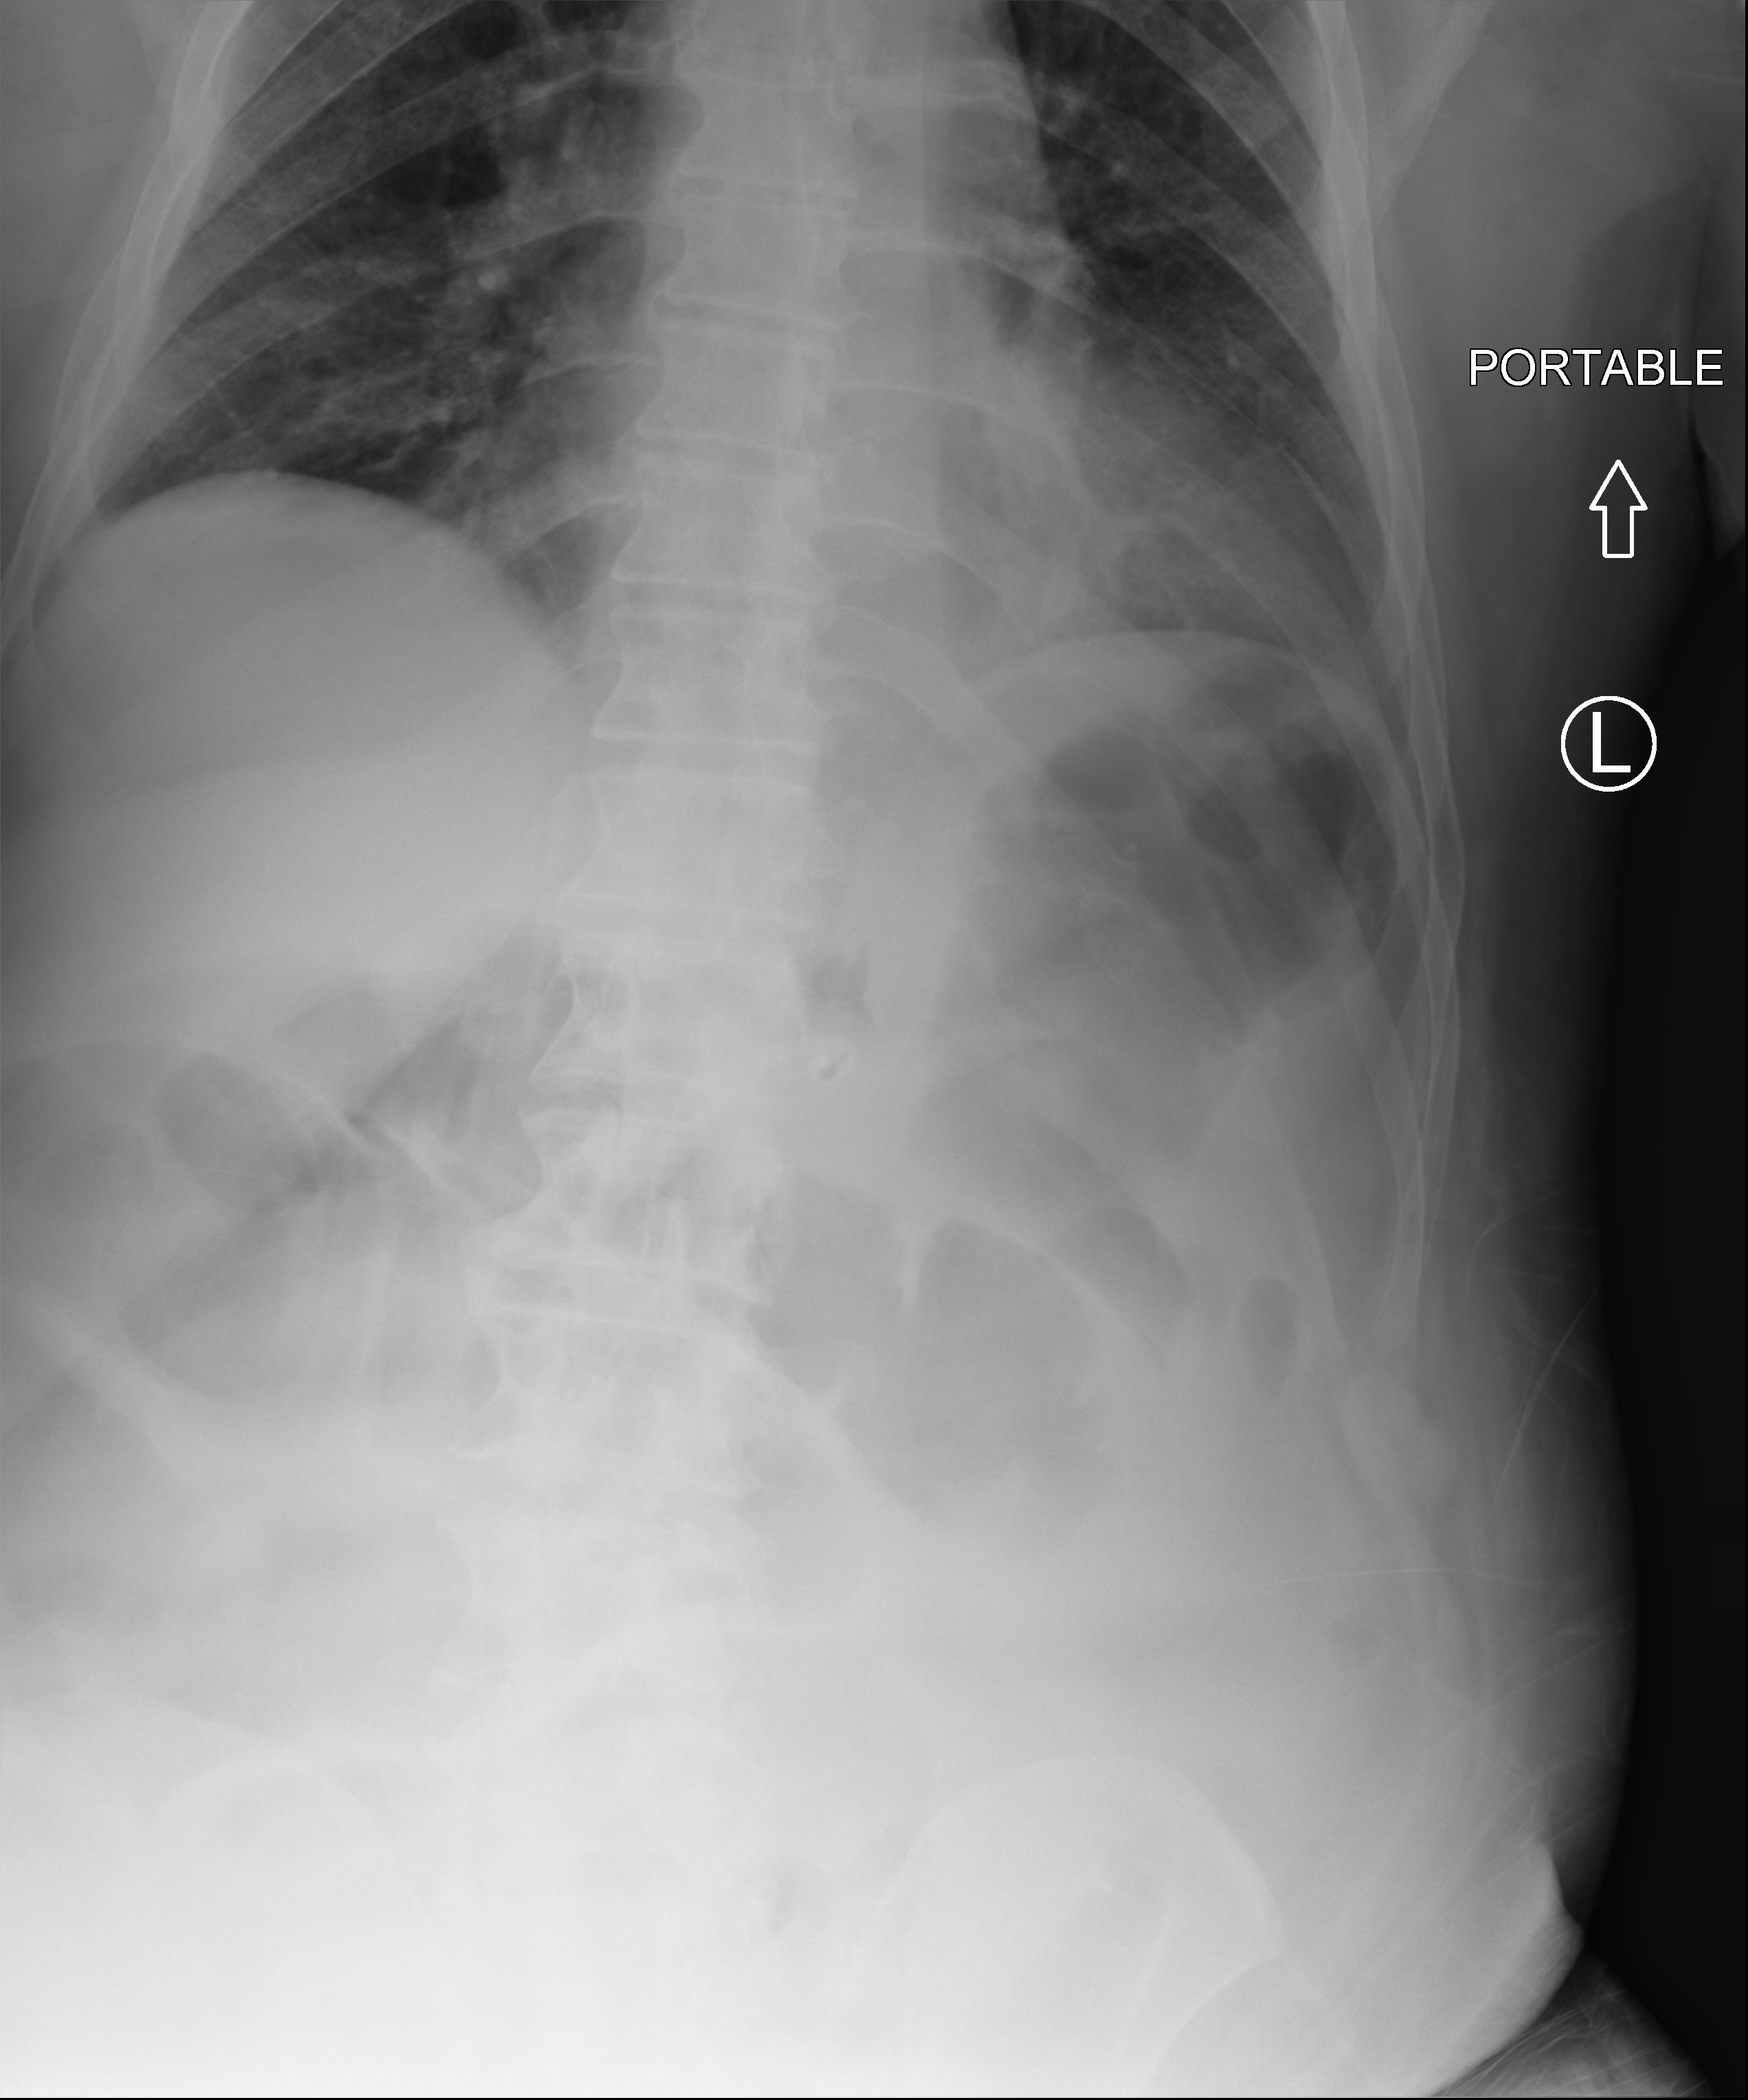
Portable abdomen radiograph, anteroposterior (AP) projection. Patient hospitalised with COVID-19; male, aged 60–74 years.
Hospital-stay facts (about this admission, not read from this image; timing relative to this image not recorded):
- mechanically ventilated during this hospital stay: no